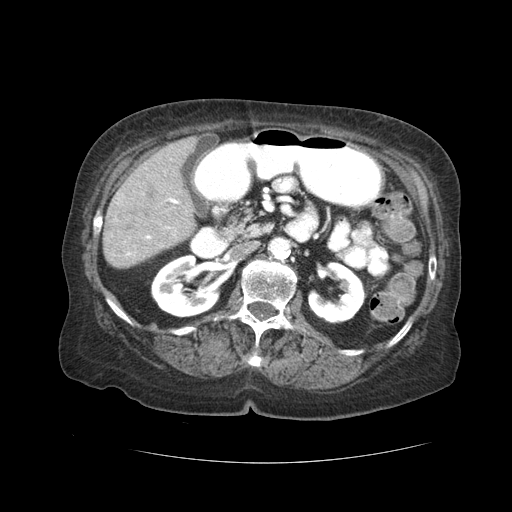
Contrast-enhanced abdominal CT (liver protocol), one axial slice. Position 8 of 59 along the scan axis. Soft-tissue window (W 400 / L 40 HU). 512 × 512 image matrix. Case-level facts recorded for this patient, not image findings: diagnosis: hepatocellular carcinoma (patient treated with transarterial chemoembolisation; whether this scan precedes or follows treatment is not stated here); TNM stage (as recorded): Stage-I; Child-Pugh class: A.
Outlined on this slice (semi-automatically segmented with operator editing):
- liver parenchyma outside the tumour (the mass and vessels are separate outlines, so this box may not span the whole liver): bounding box [x1, y1, x2, y2] px = [102, 136, 198, 268]
- liver vessels: [127, 198, 179, 255]